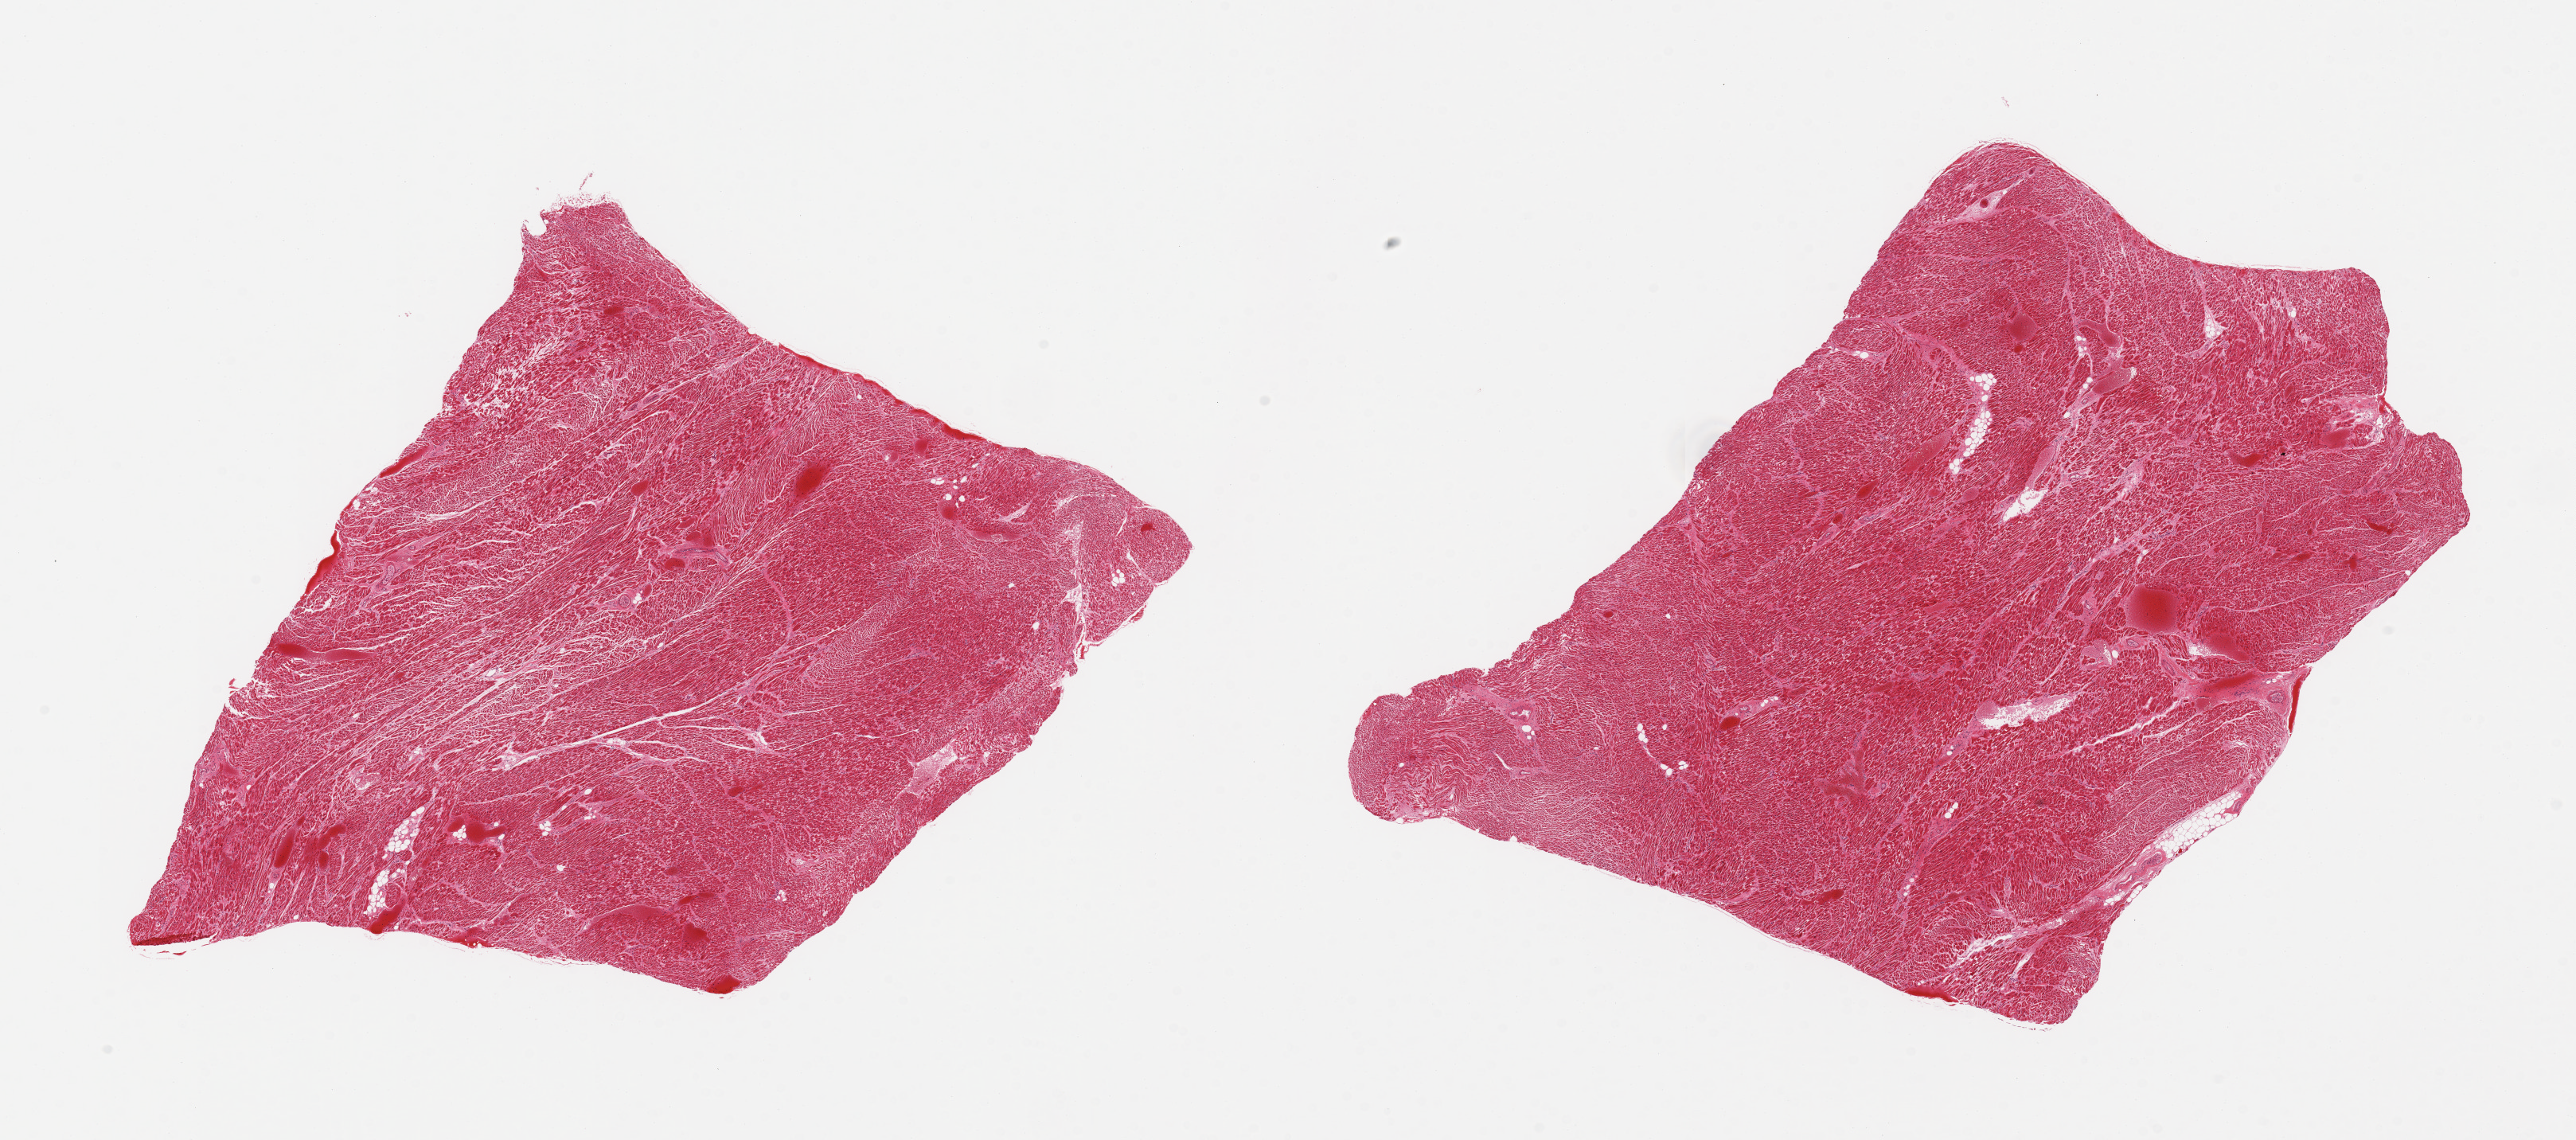
Digitized haematoxylin and eosin-stained section, brightfield, shown as a low-resolution overview of the whole scanned area (about 25.6 x 11.3 mm); PAXgene-fixed paraffin-embedded (PFPE) section; sampled site (target tissue): heart; donor tissue sample. Donor: female.
Reviewer comment on this tissue sample: 2 pieces; moderate congestion; fragmented myofibers; areas of hypereosinophilia.